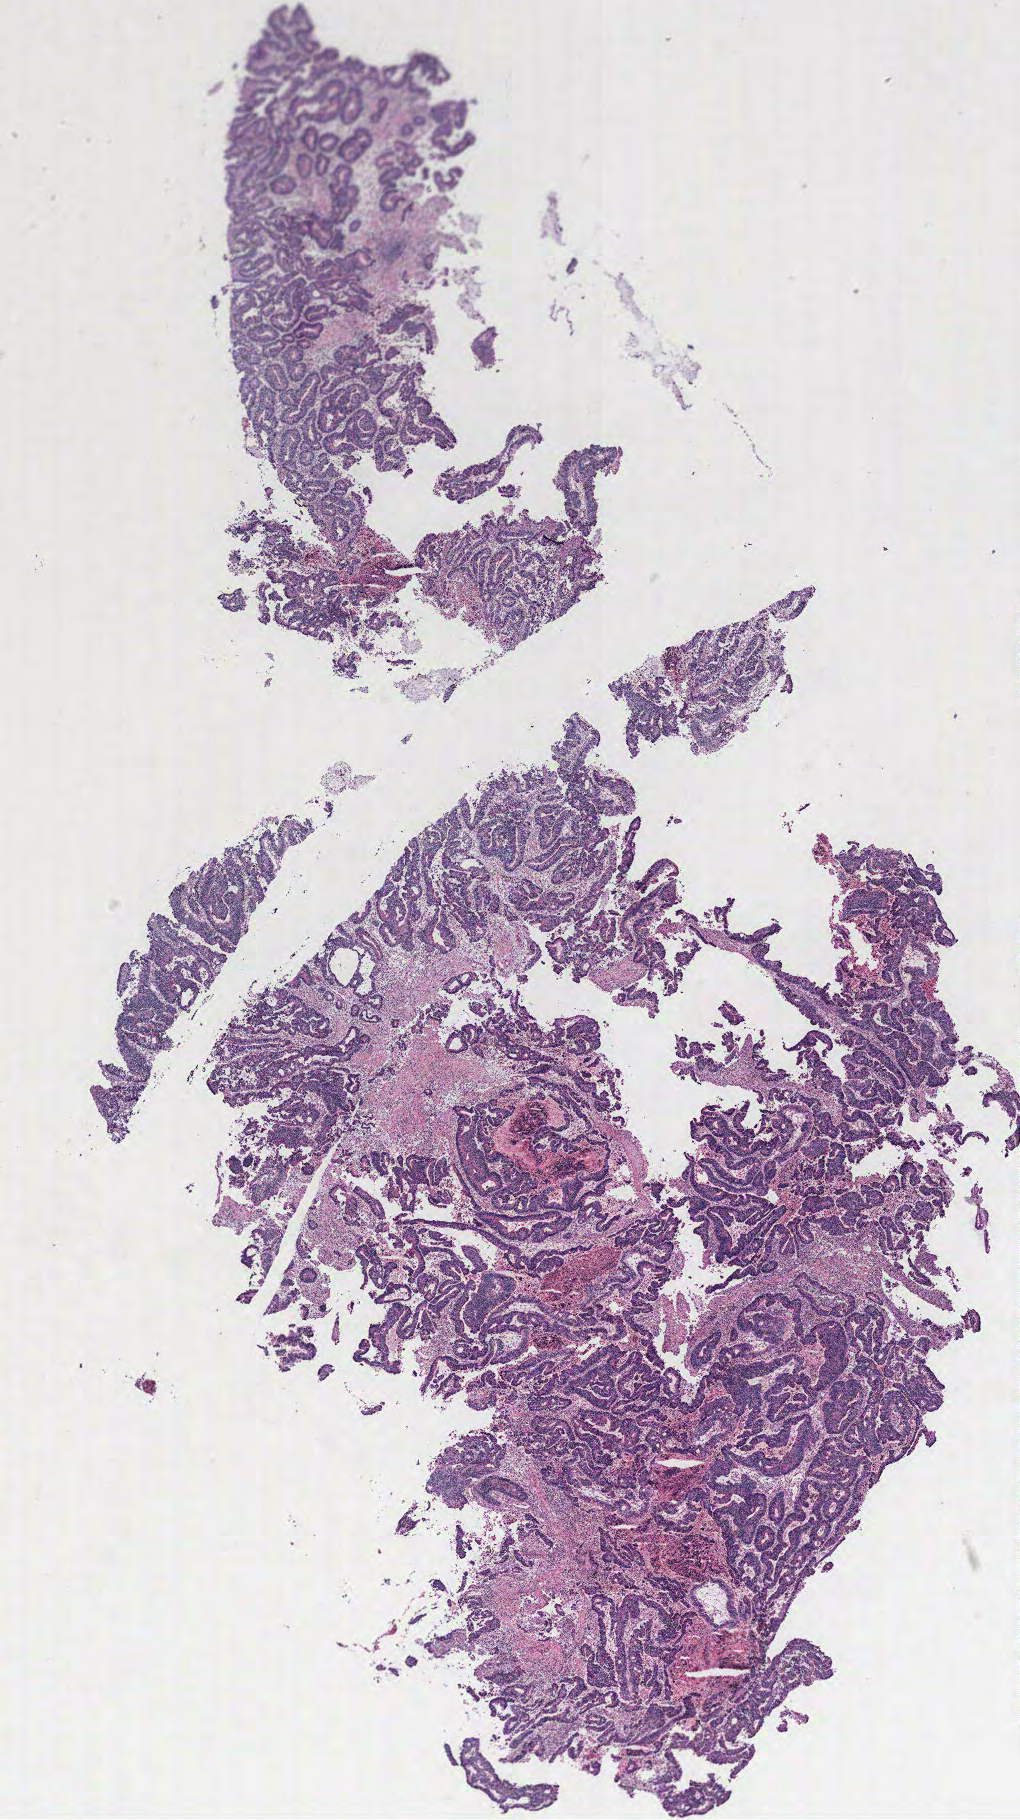
Whole-slide histology image, H&E, shown as a low-resolution overview of the whole scanned area (about 8.2 x 14.6 mm); colon, tissue type not recorded.
Patient diagnosis (cohort enrolment): colon cancer (colon).